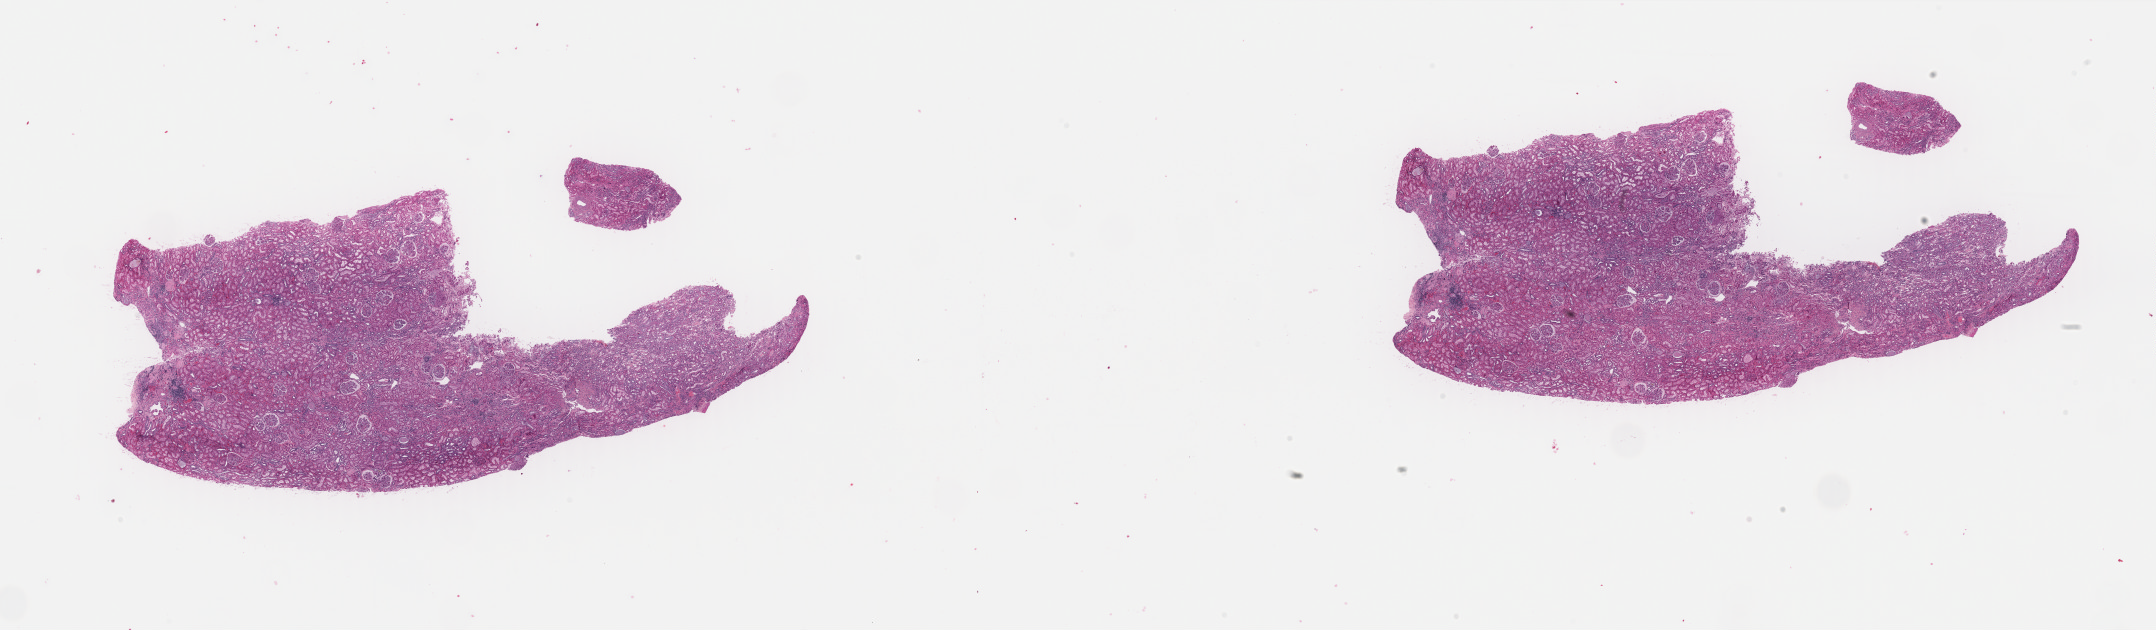
Digitized Hematoxylin and eosin (H&E) stained tissue section (whole slide) — low-resolution overview of the scanned area, about 34.1 x 10.0 mm (from a 40x scan). Formalin-fixed paraffin-embedded (FFPE) diagnostic section. Kidney, solid tissue normal (non-tumour tissue) sample. Female, age 75 years at initial diagnosis. Pathologist review of this section (percent, as recorded): tumour cells 0%, tumour nuclei 0%, normal cells 80%, stromal cells 20%, necrosis 0%. Infiltration values recorded for this section: lymphocyte infiltration 4%, monocyte infiltration 1%, neutrophil infiltration 1%.
- this section: solid tissue normal sample (biorepository sample class)
- patient diagnosis: Renal cell carcinoma, chromophobe type